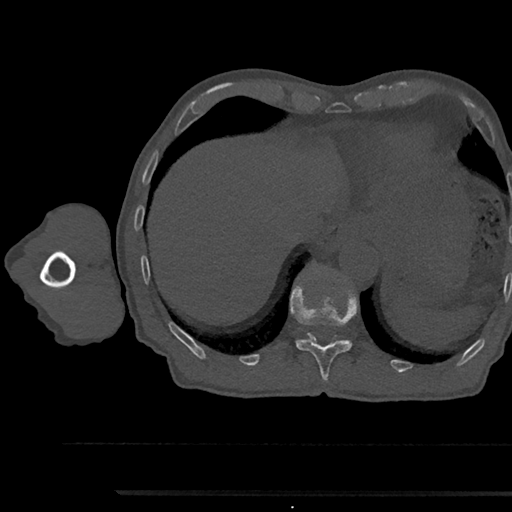
CT including the spine, one axial slice. Position 770 of 797 along the scan axis. Reconstruction kernel Br40s/3. Bone window (W 1800 / L 400 HU). 0.5 mm slice thickness. 512 × 512 image matrix, field of view 367 × 367 mm. Patient: male, 79 years. Case-level facts recorded for this patient, not image findings: primary cancer: prostate.
Outlined on this slice (semi-automatic segmentation, software-assisted and operator-edited):
- T11 vertebra: box from (x=291, y=288) to (x=356, y=381) px
- T12 vertebra: (x=308, y=334)–(x=311, y=337)